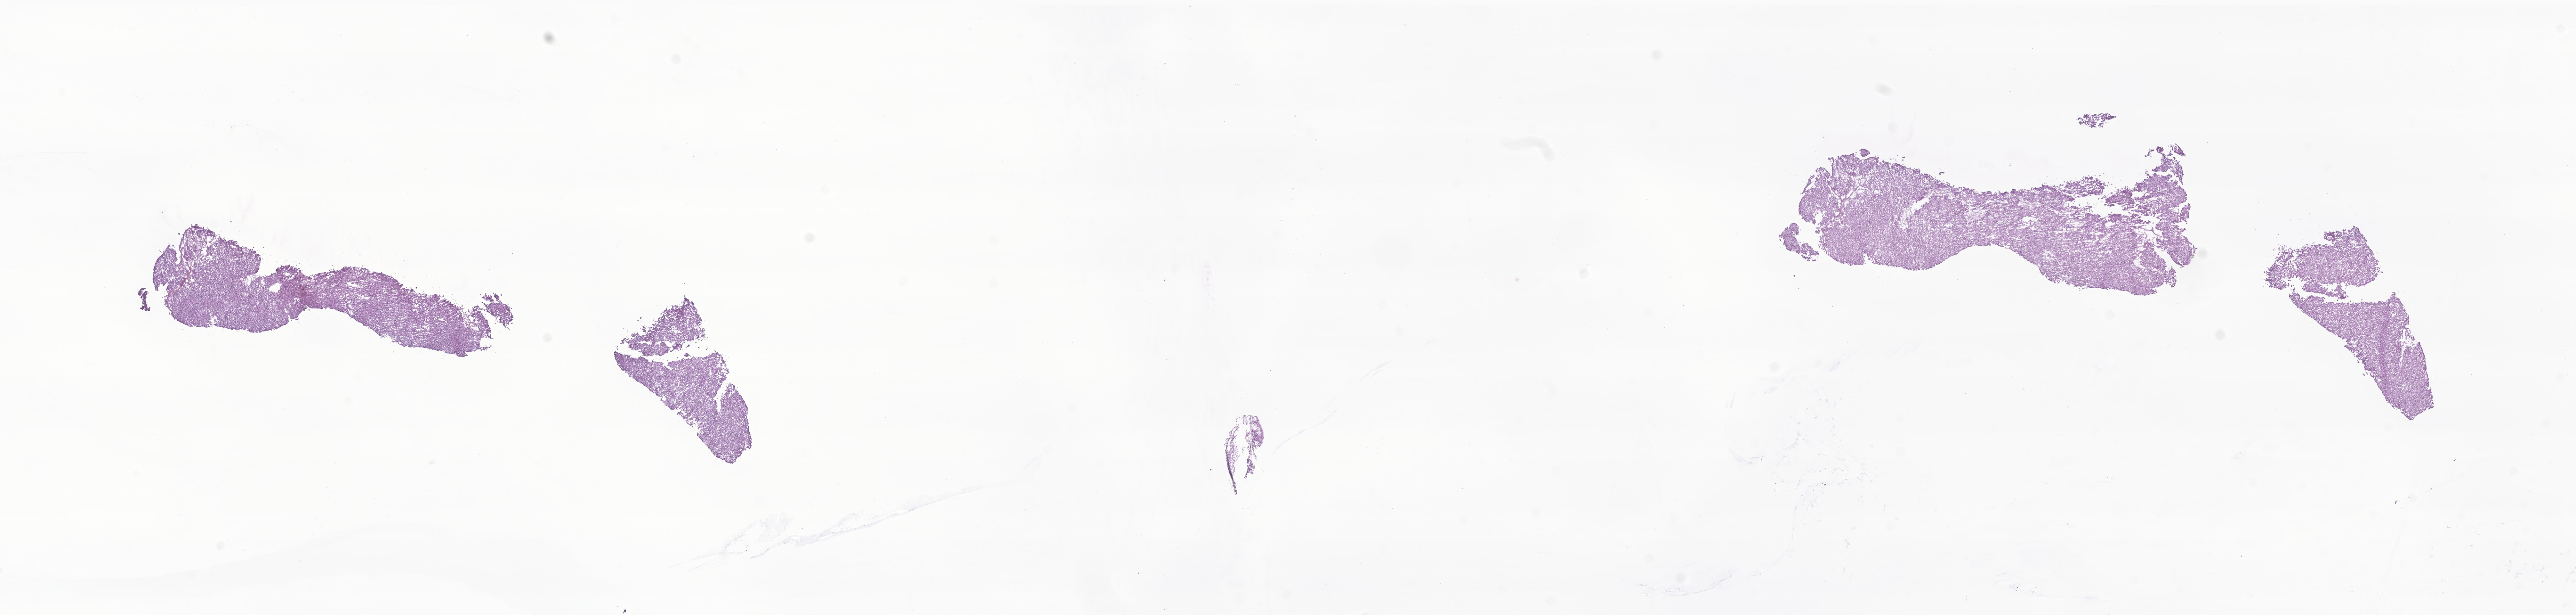
Digitized haematoxylin and eosin-stained section of tumor tissue from the abdomen, whole scanned area (about 33.9 x 8.1 mm) shown as a low-resolution overview; cryosection (OCT / tissue freezing medium). Patient female; age 192 months (16 years).
* diagnosis (ICD-O-3 morphology term): Gastrointestinal stromal tumor, NOS